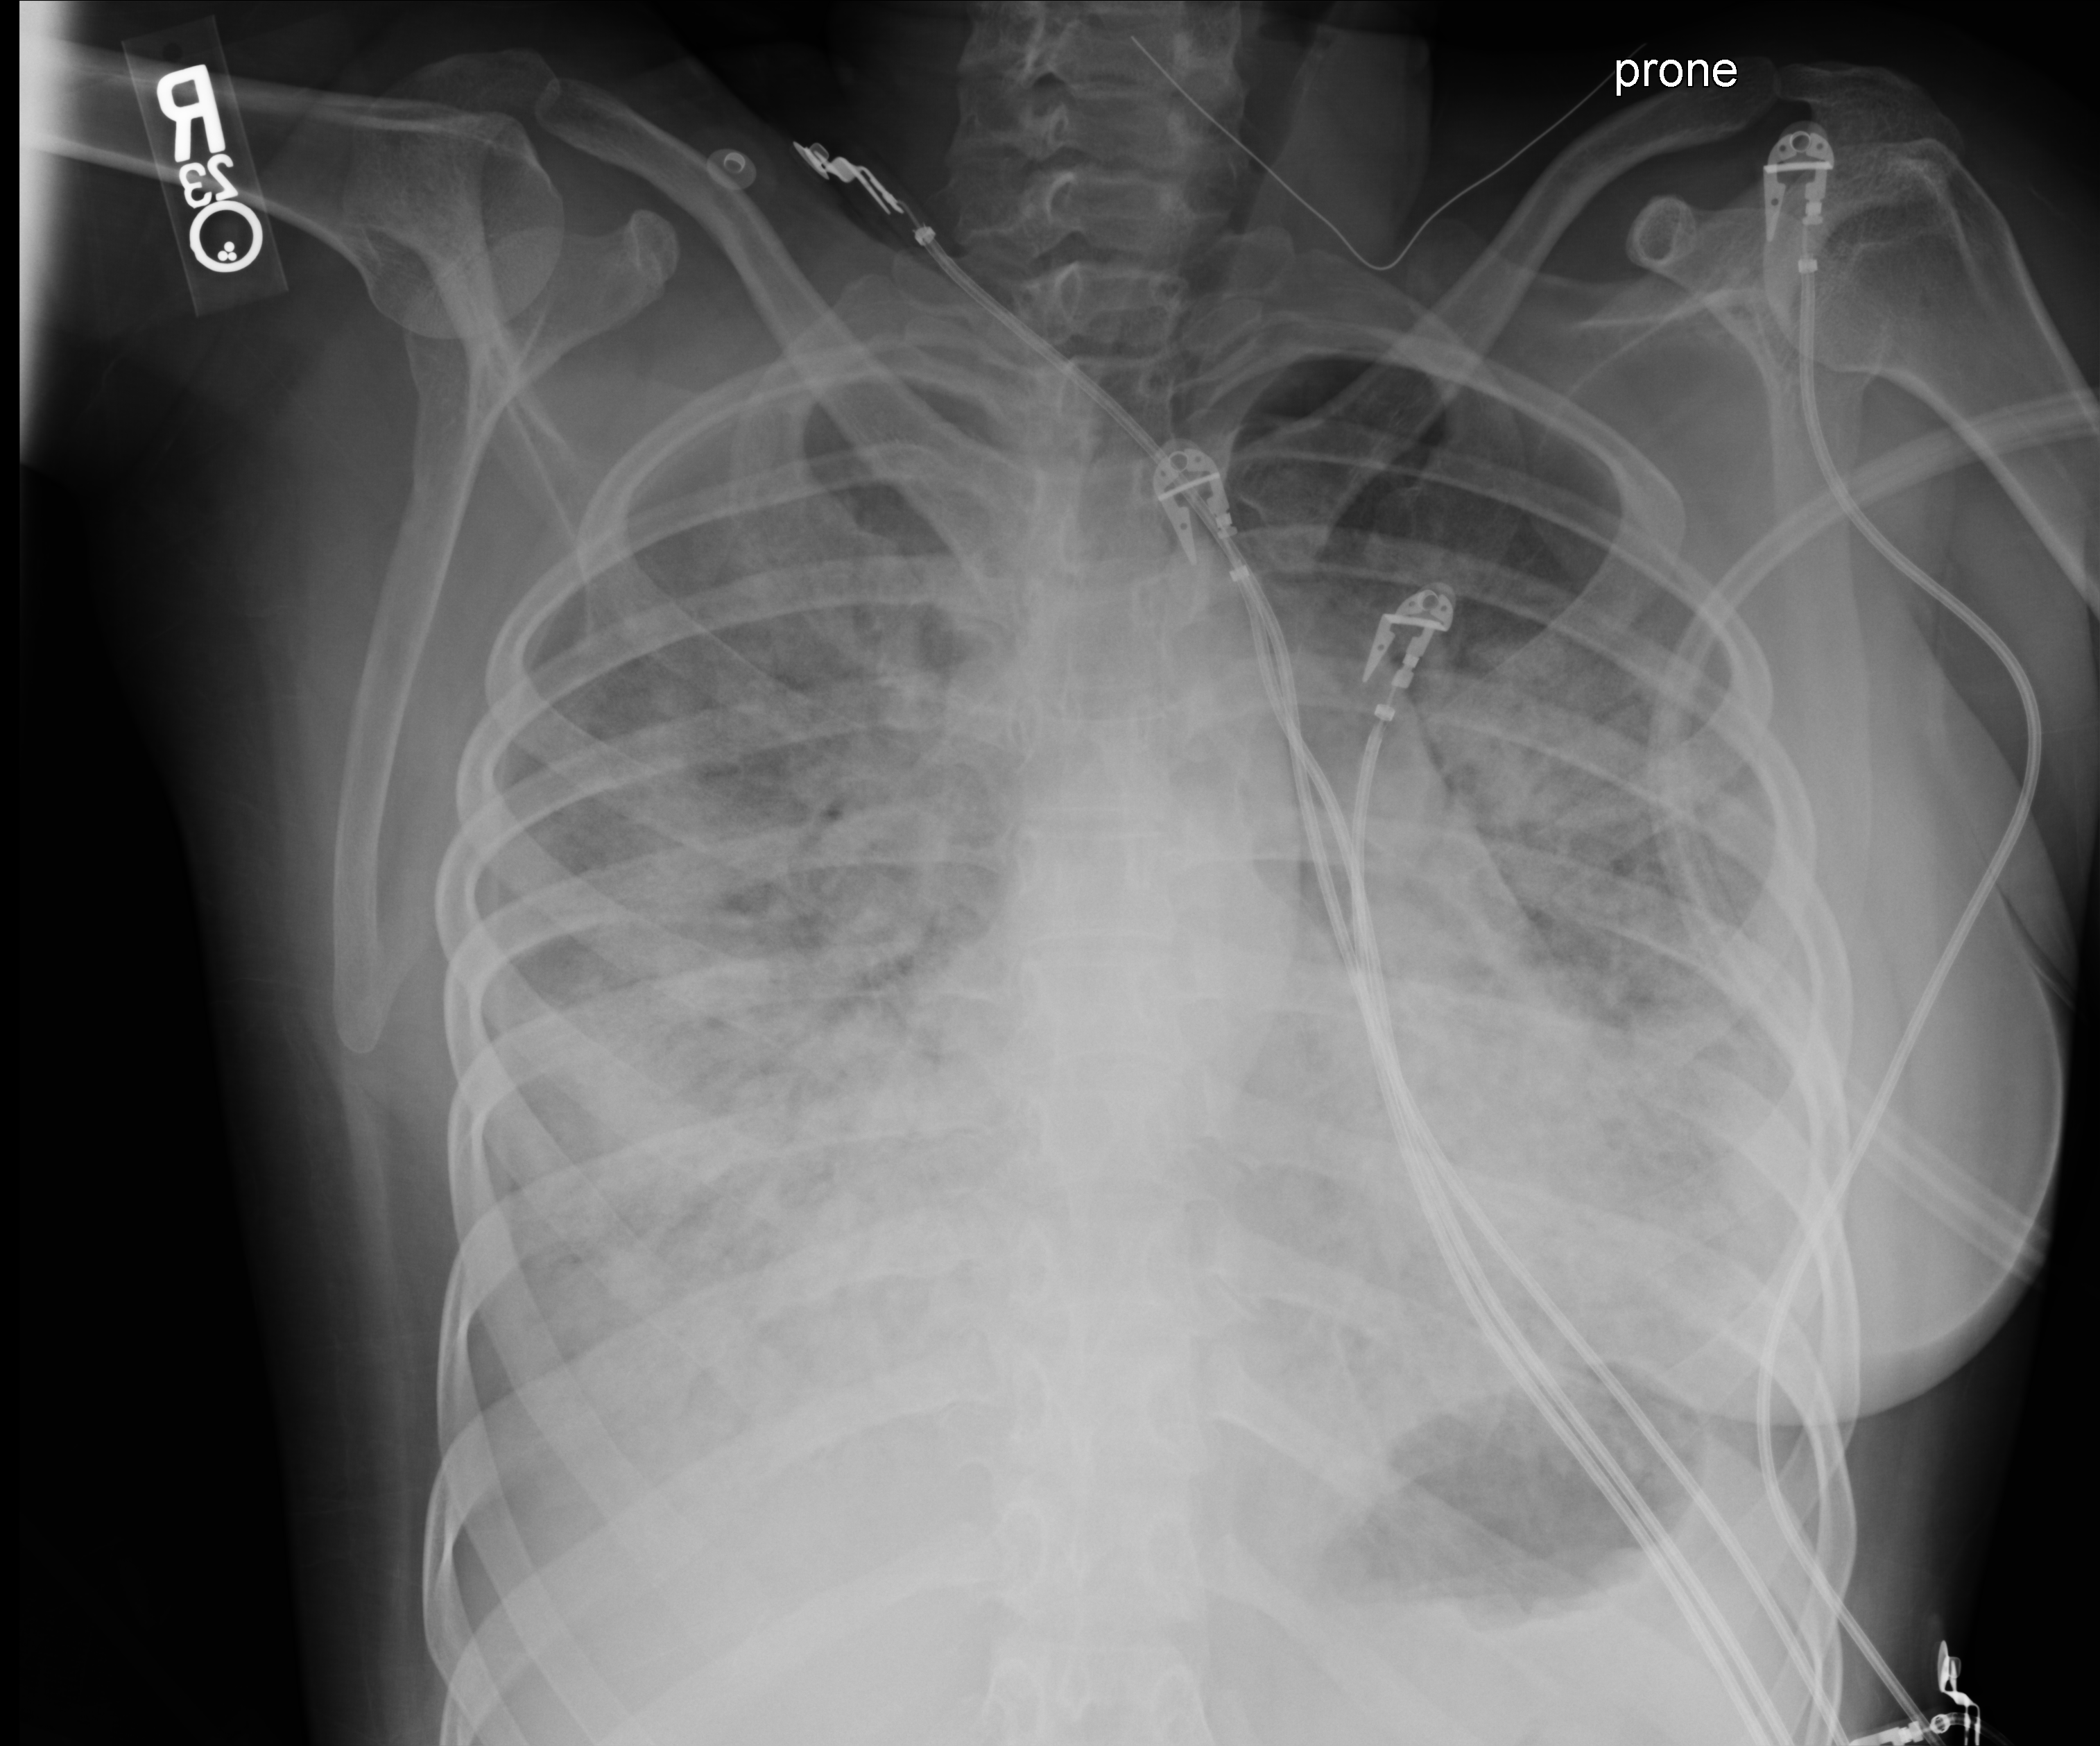
Portable chest radiograph, anteroposterior (AP) projection. Patient hospitalised with COVID-19, aged 18–59 years.
From the hospital-stay record, not from the radiograph (when in the stay this image was taken is not recorded): mechanically ventilated during this hospital stay: yes; admitted to intensive care during this hospital stay: yes; length of hospital stay: 30 days.